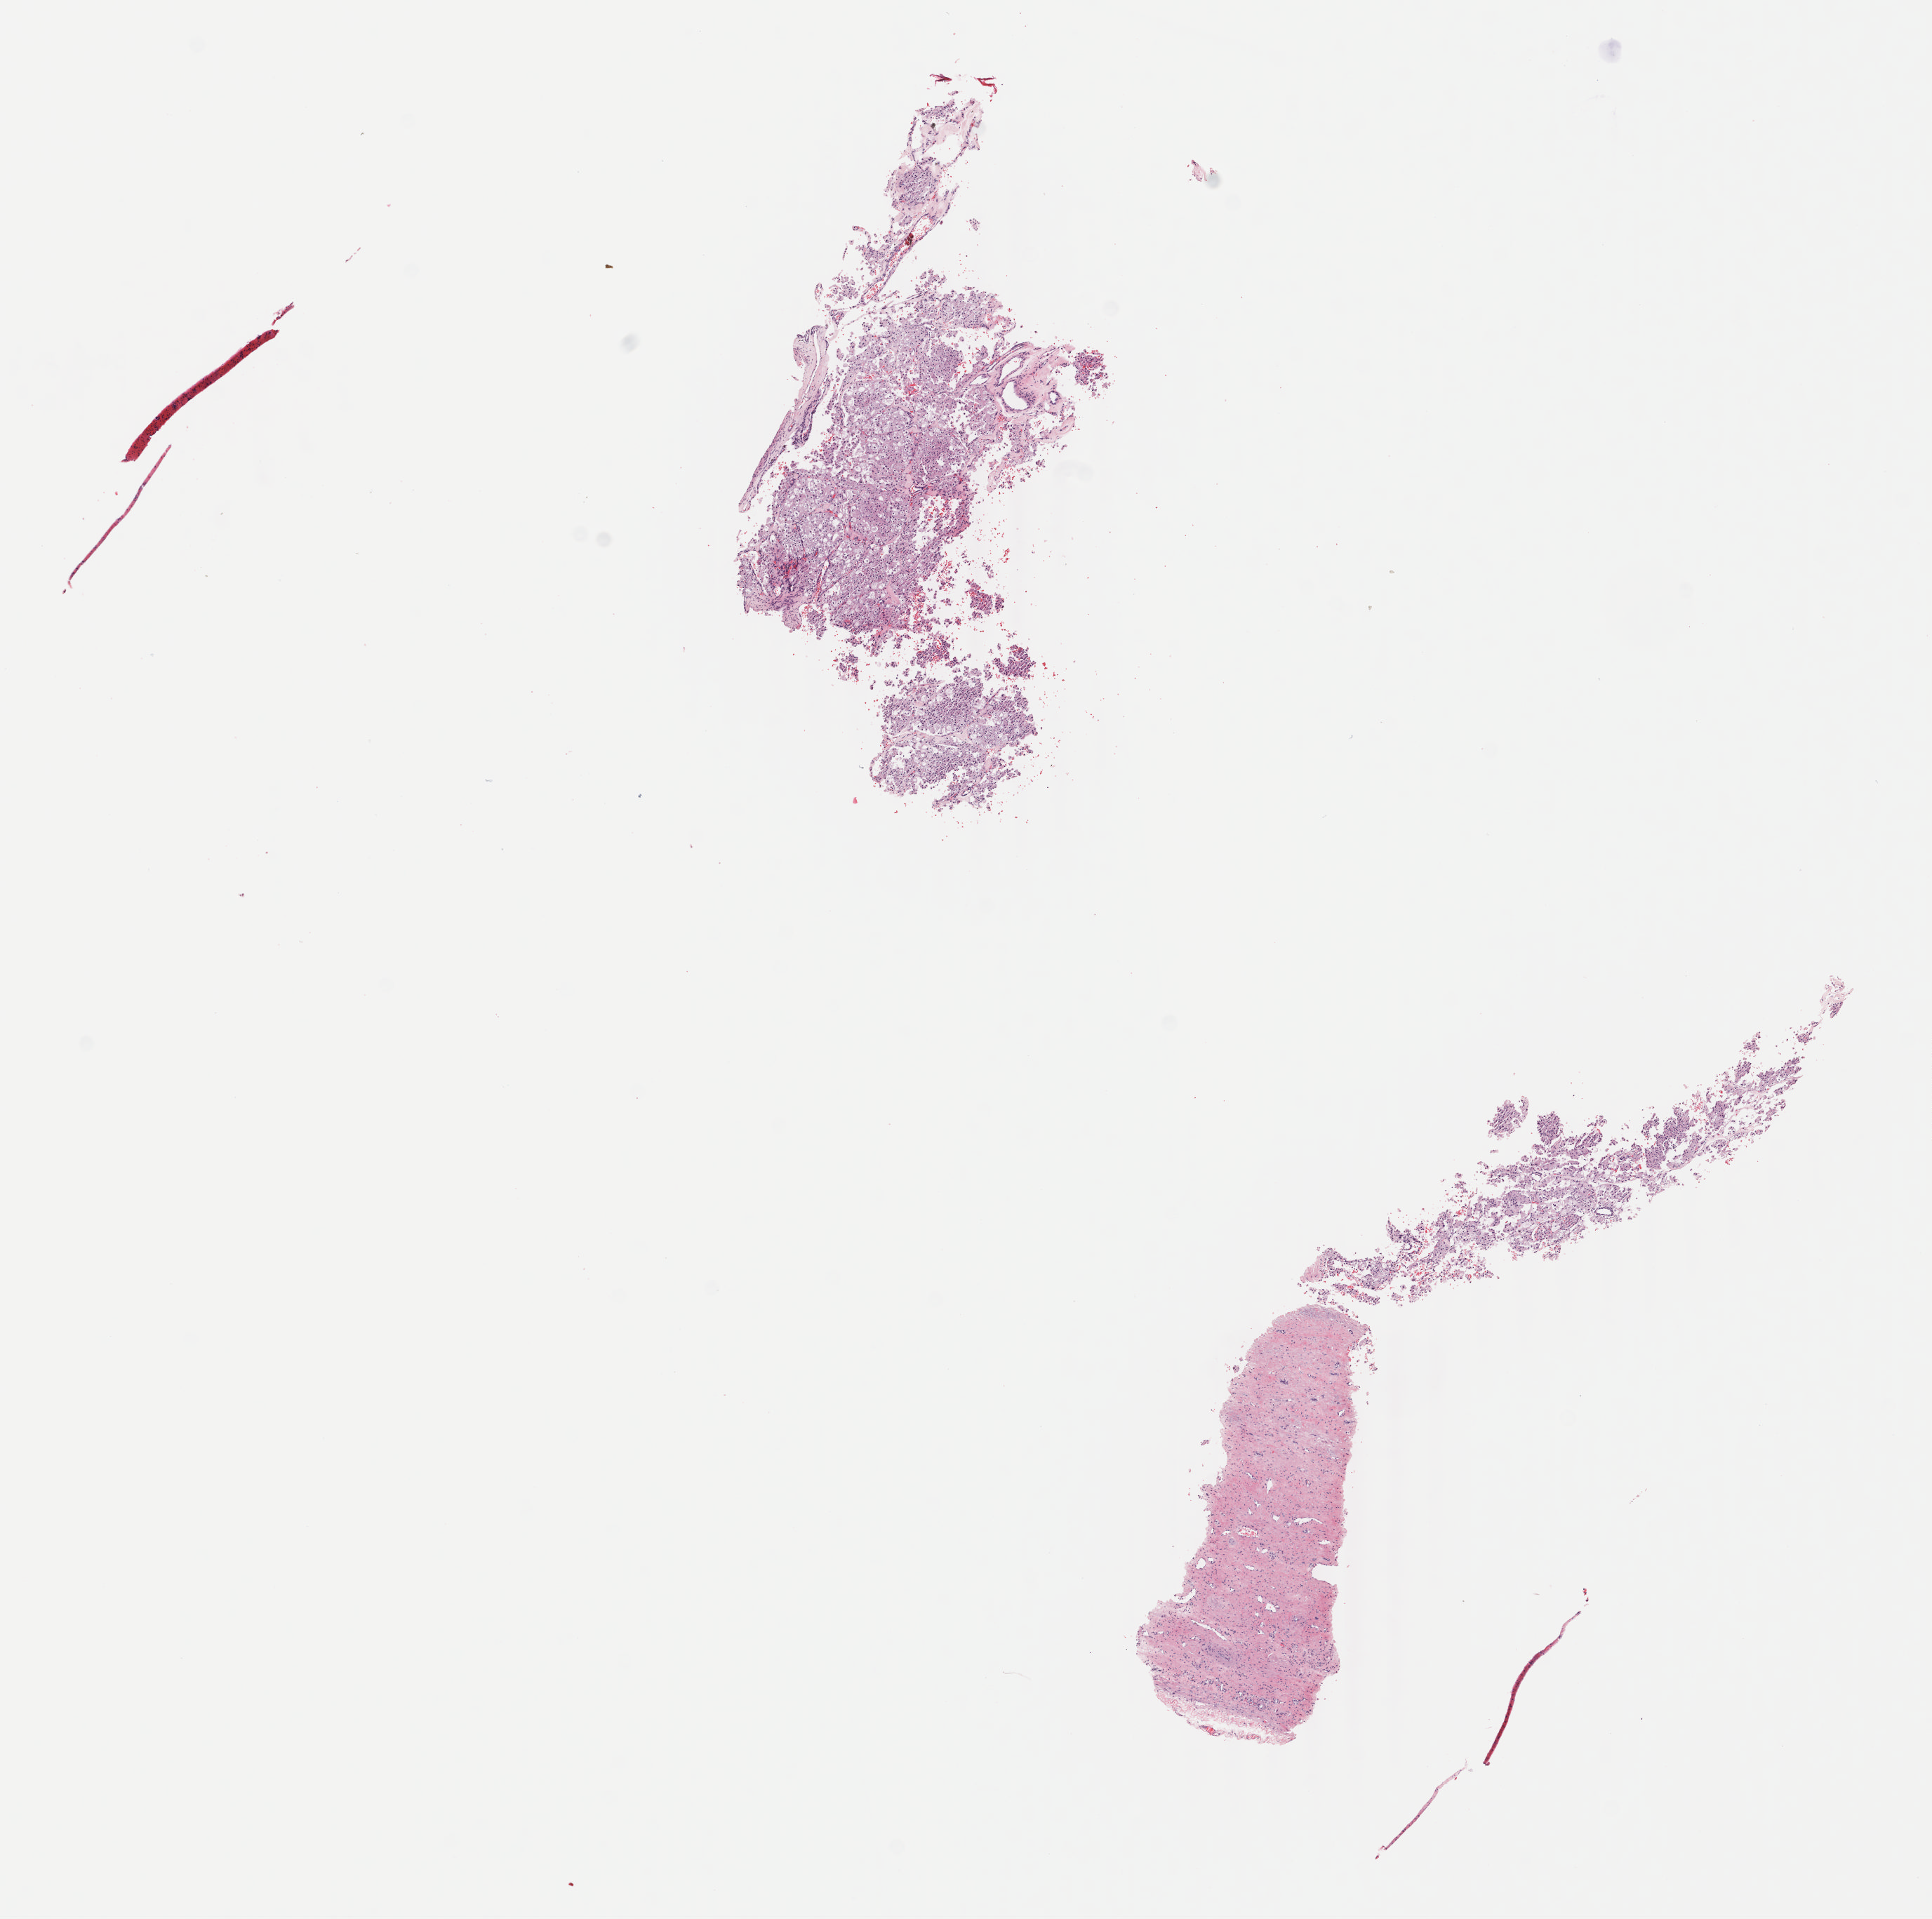
Whole-slide histology image, H&E, whole scanned area (about 10.9 x 10.9 mm) shown as a low-resolution overview; frozen section from the bottom of the tissue portion; primary tumour sample from the kidney. Male, age 59 years at initial diagnosis. Histologic grade: G2 (moderately differentiated). Composition of this section per pathologist review: tumour cells 60%, tumour nuclei 70%, normal cells 0%, stromal cells 40%, necrosis 0%. Inflammatory infiltration, as recorded: lymphocyte infiltration 1%, monocyte infiltration 1%, neutrophil infiltration 0%.
AJCC pathologic stage: II. Pathologic diagnosis: Clear cell adenocarcinoma, NOS.